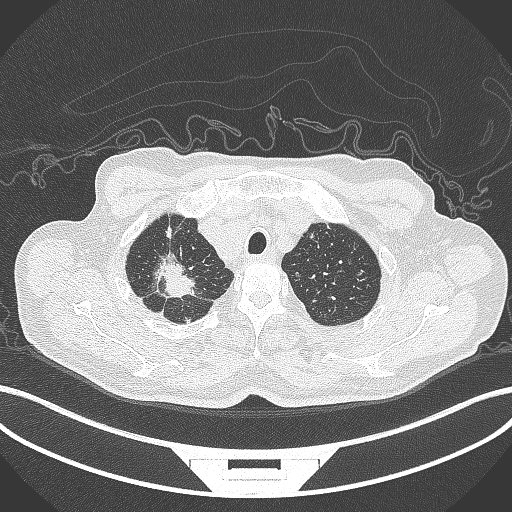
Chest CT, one axial slice. Position 336 of 407 along the scan axis. Lung window (W 1500 / L -600 HU). 1 mm slice thickness. 512 × 512 image matrix, field of view 400 × 400 mm. Male patient, age 69 years. Case-level facts recorded for this patient, not image findings: clinical TNM (as recorded): T1c N1 M1.
Annotated regions visible in this slice (rectangle marked by the reading radiologist):
- lung tumour (recorded histology: adenocarcinoma): bounding box [x1, y1, x2, y2] px = [151, 246, 202, 307]